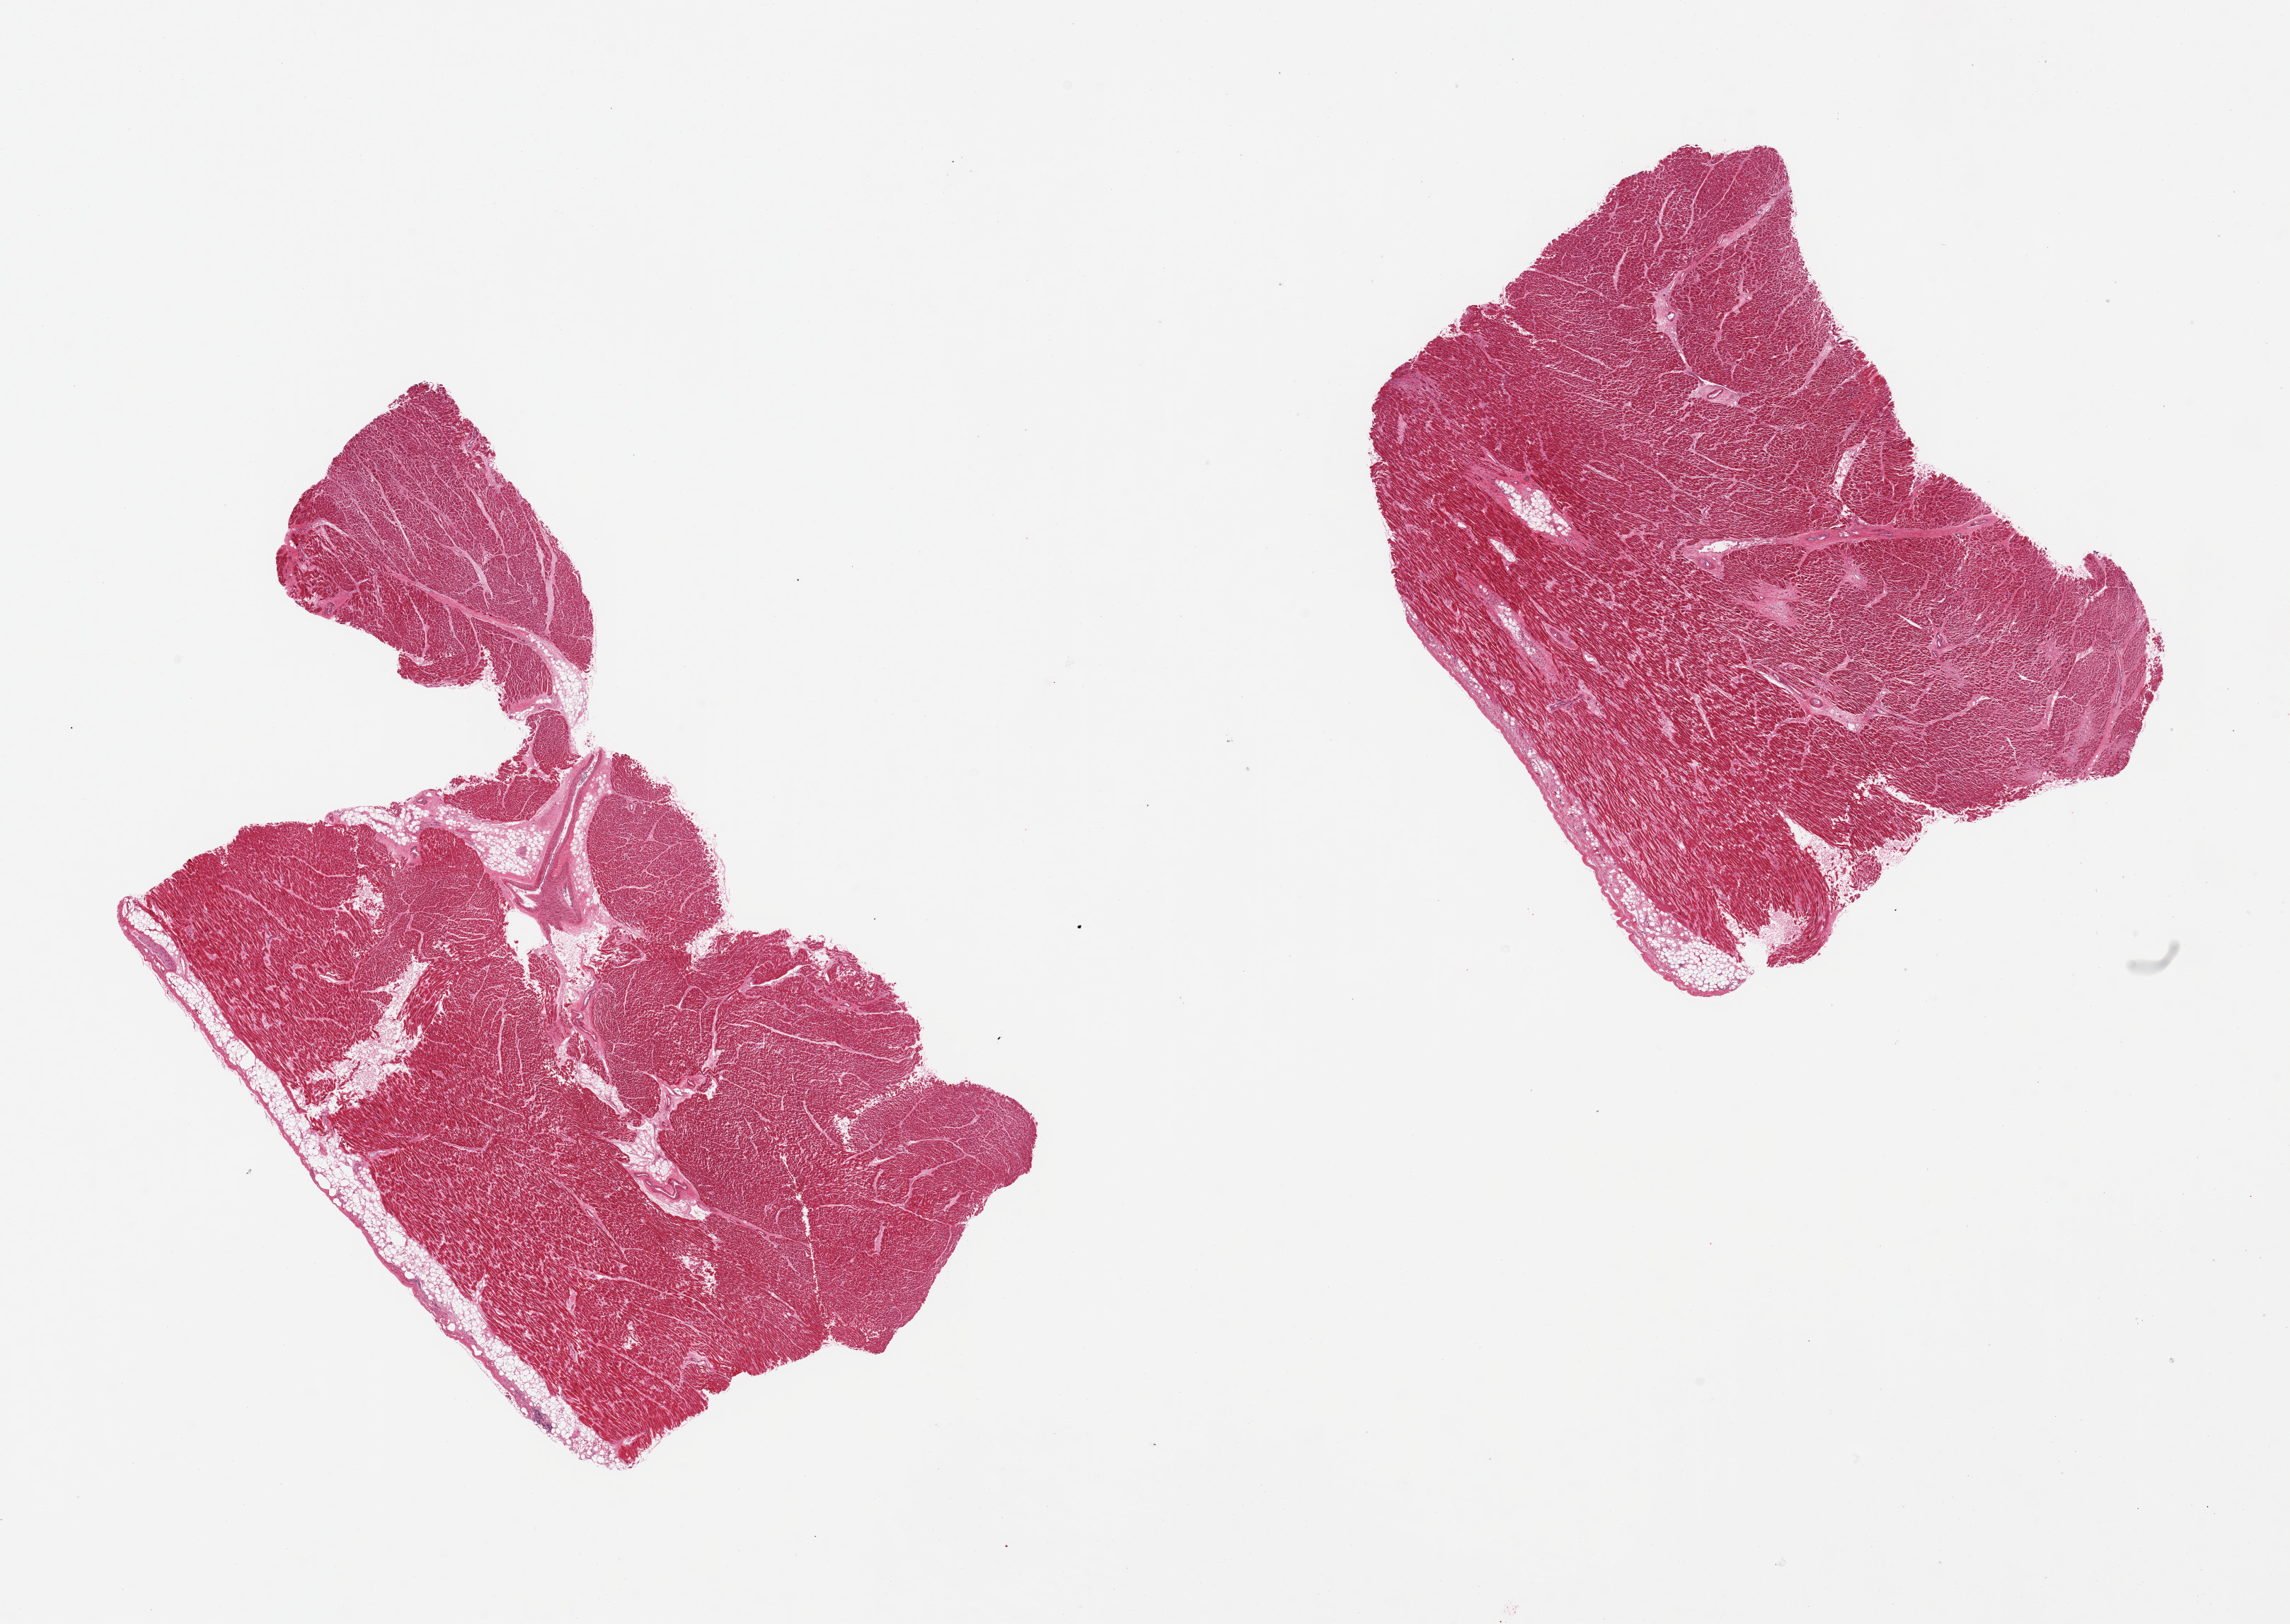
Whole-slide image, hematoxylin and eosin (H&E) stain, low-resolution overview of the scanned area, about 25.6 x 18.2 mm (slide scanned at 20x), PAXgene-fixed paraffin-embedded (PFPE) section, section of heart (target tissue), donor tissue sample. Male donor.
Reviewer comment on this tissue sample: 2 pieces, some attached and internal fat (<10%) and interstitial and patchy fibrosis.